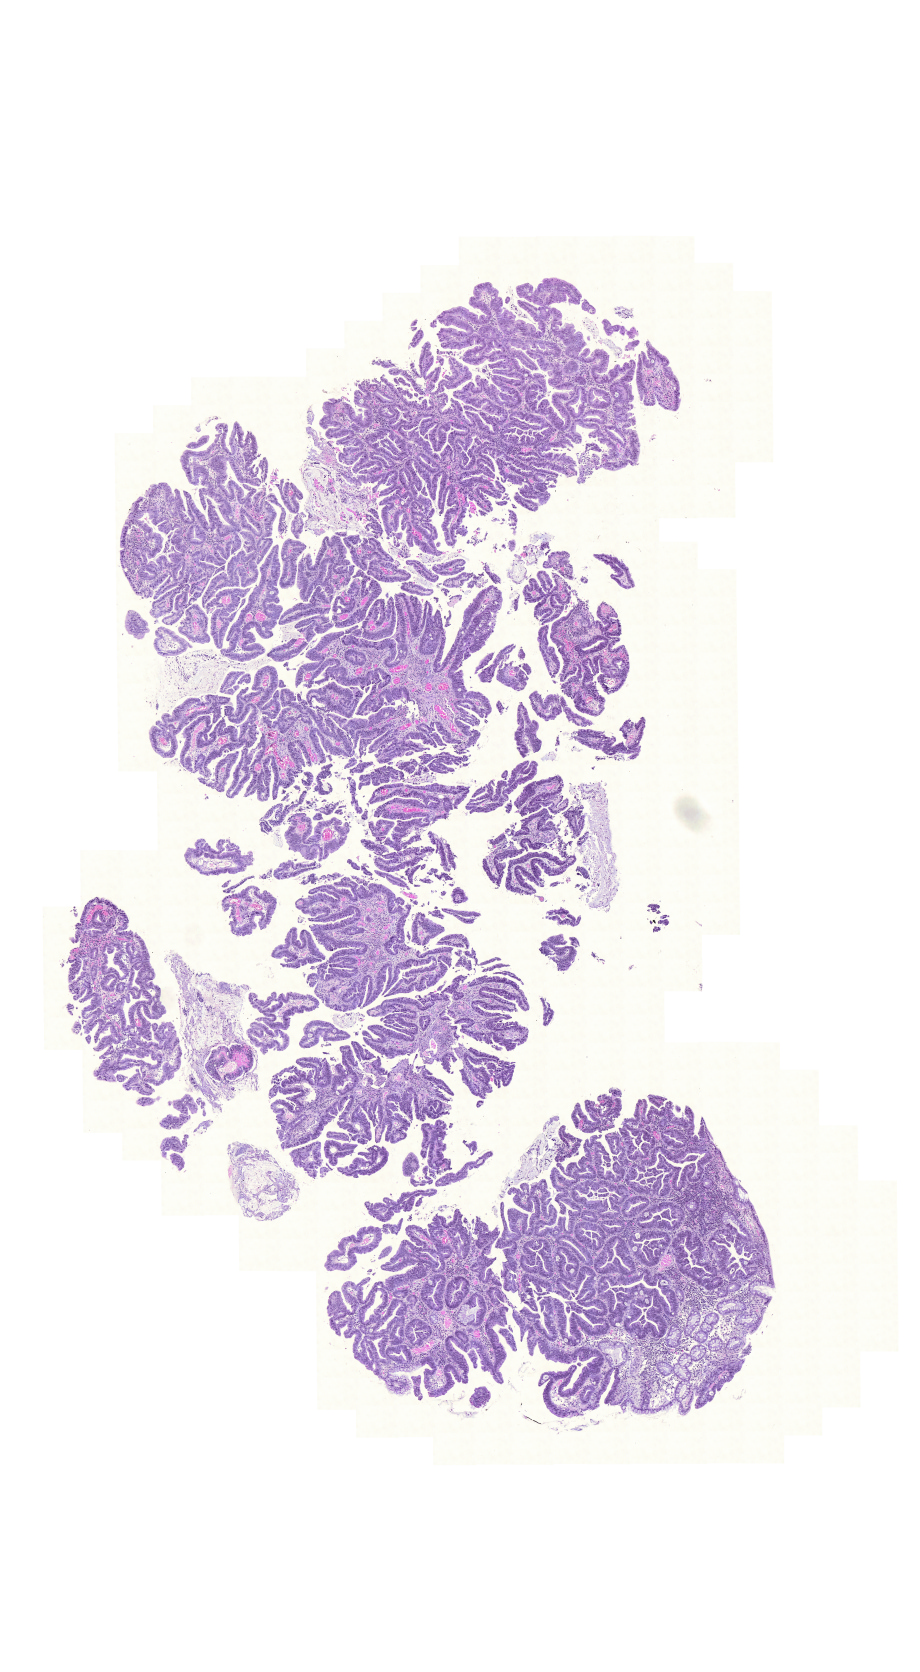
H&E whole-slide image — shown as a low-resolution overview of the whole scanned area (about 6.8 x 12.4 mm). Formalin-fixed paraffin-embedded (FFPE) diagnostic section. Sample: primary tumour, rectum. Patient: male, age at initial diagnosis 77 years.
AJCC pathologic stage: I. Lymph nodes positive (case pathology): 0 of 15 examined. Diagnosis: Adenocarcinoma, NOS.